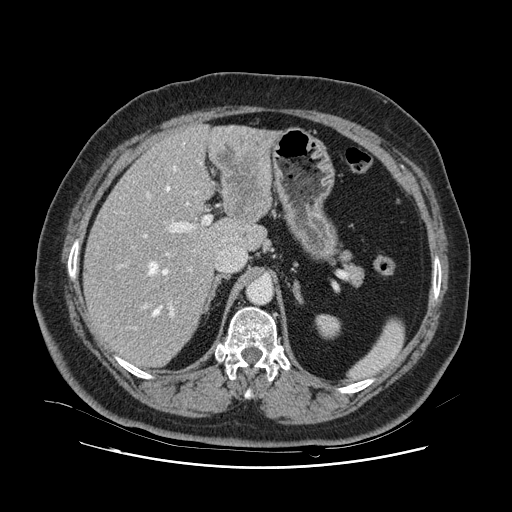
Contrast-enhanced abdominal CT, one axial slice; position 72 of 132 along the scan axis; 120 kVp; intravenous contrast given; soft-tissue window (W 400 / L 40 HU); 512 × 512 image matrix, field of view 391 × 391 mm. Female patient, age 73 years. From the clinical record (not read from this slice): diagnosis: colorectal cancer liver metastases, imaged before liver resection; multiple liver metastases: no; largest metastasis: 7 cm; disease in both lobes: no.
Annotated regions visible in this slice (outlined manually by an expert reader):
- hepatic veins: bounding box (x1, y1, x2, y2) in pixels: (132, 143, 197, 329)
- liver: (84, 126, 273, 367)
- planned liver remnant (the part of the liver to remain after resection): (85, 156, 242, 367)
- portal vein (with intrahepatic branches): (118, 194, 212, 317)
- liver metastasis: (219, 138, 265, 220)